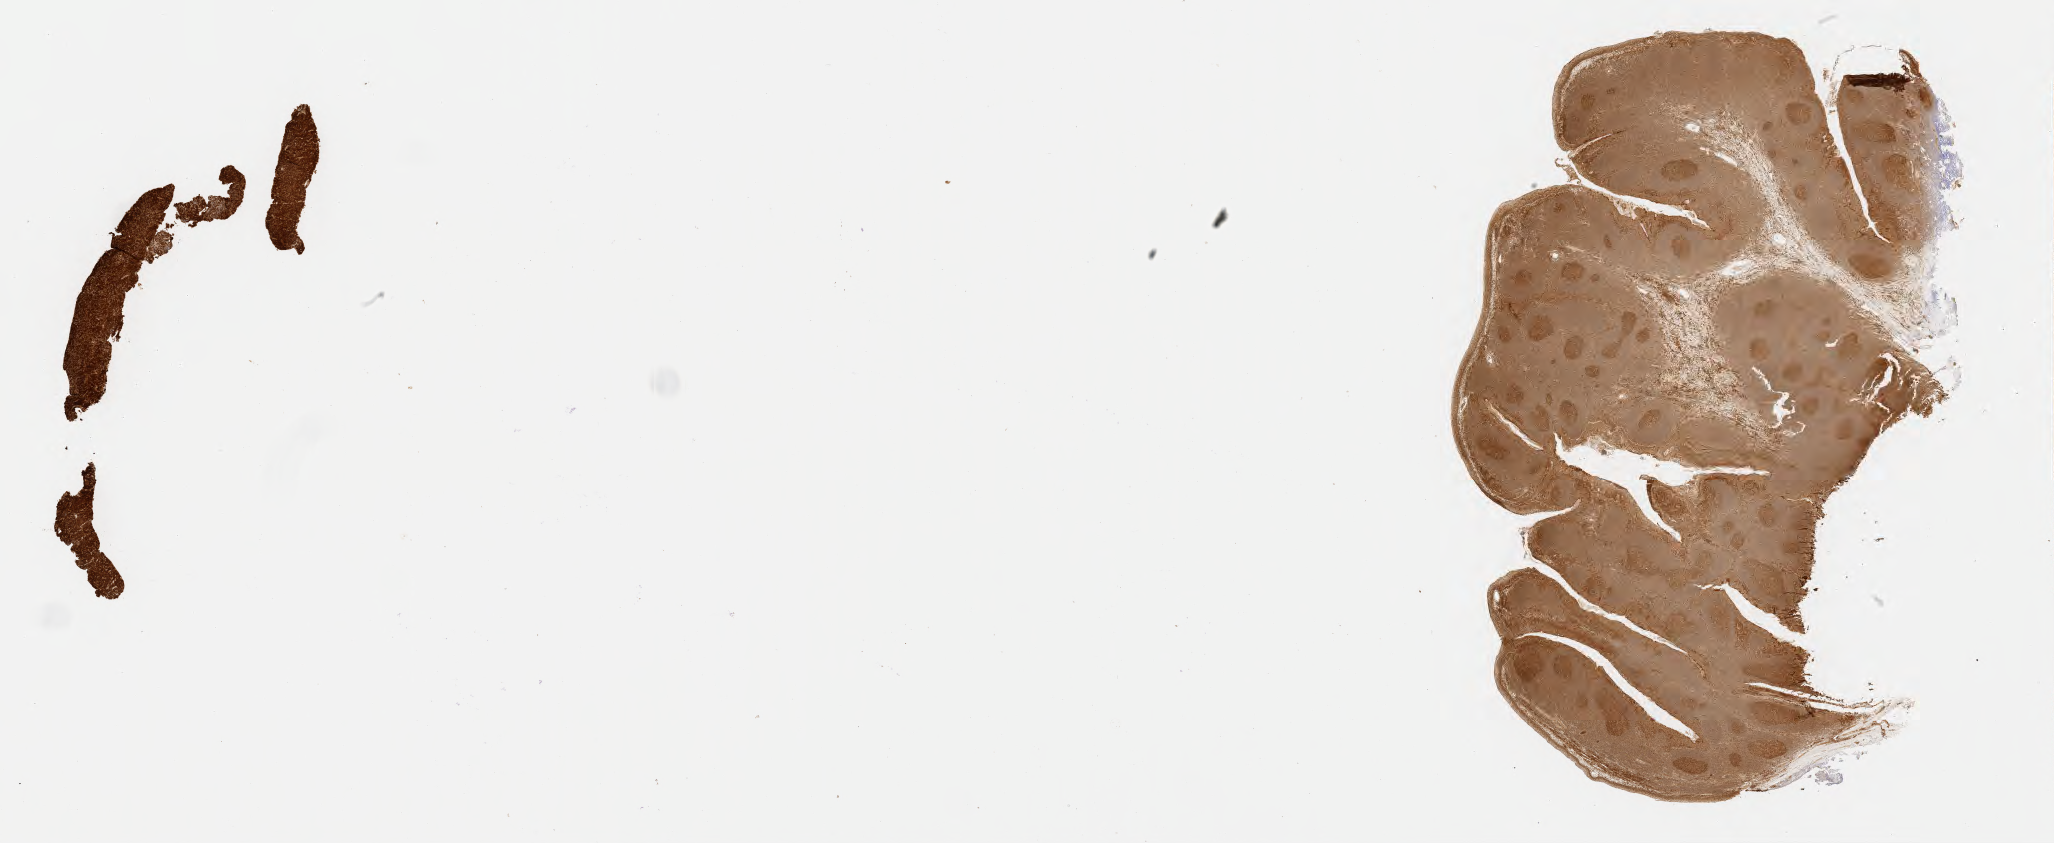
Immunohistochemistry (IHC) whole-slide image stained for BCL6 — whole scanned area (about 33.2 x 13.6 mm) shown as a low-resolution overview; tumor tissue. Patient male; 10 years old.
Diagnosis: Diffuse large B-cell lymphoma, NOS.